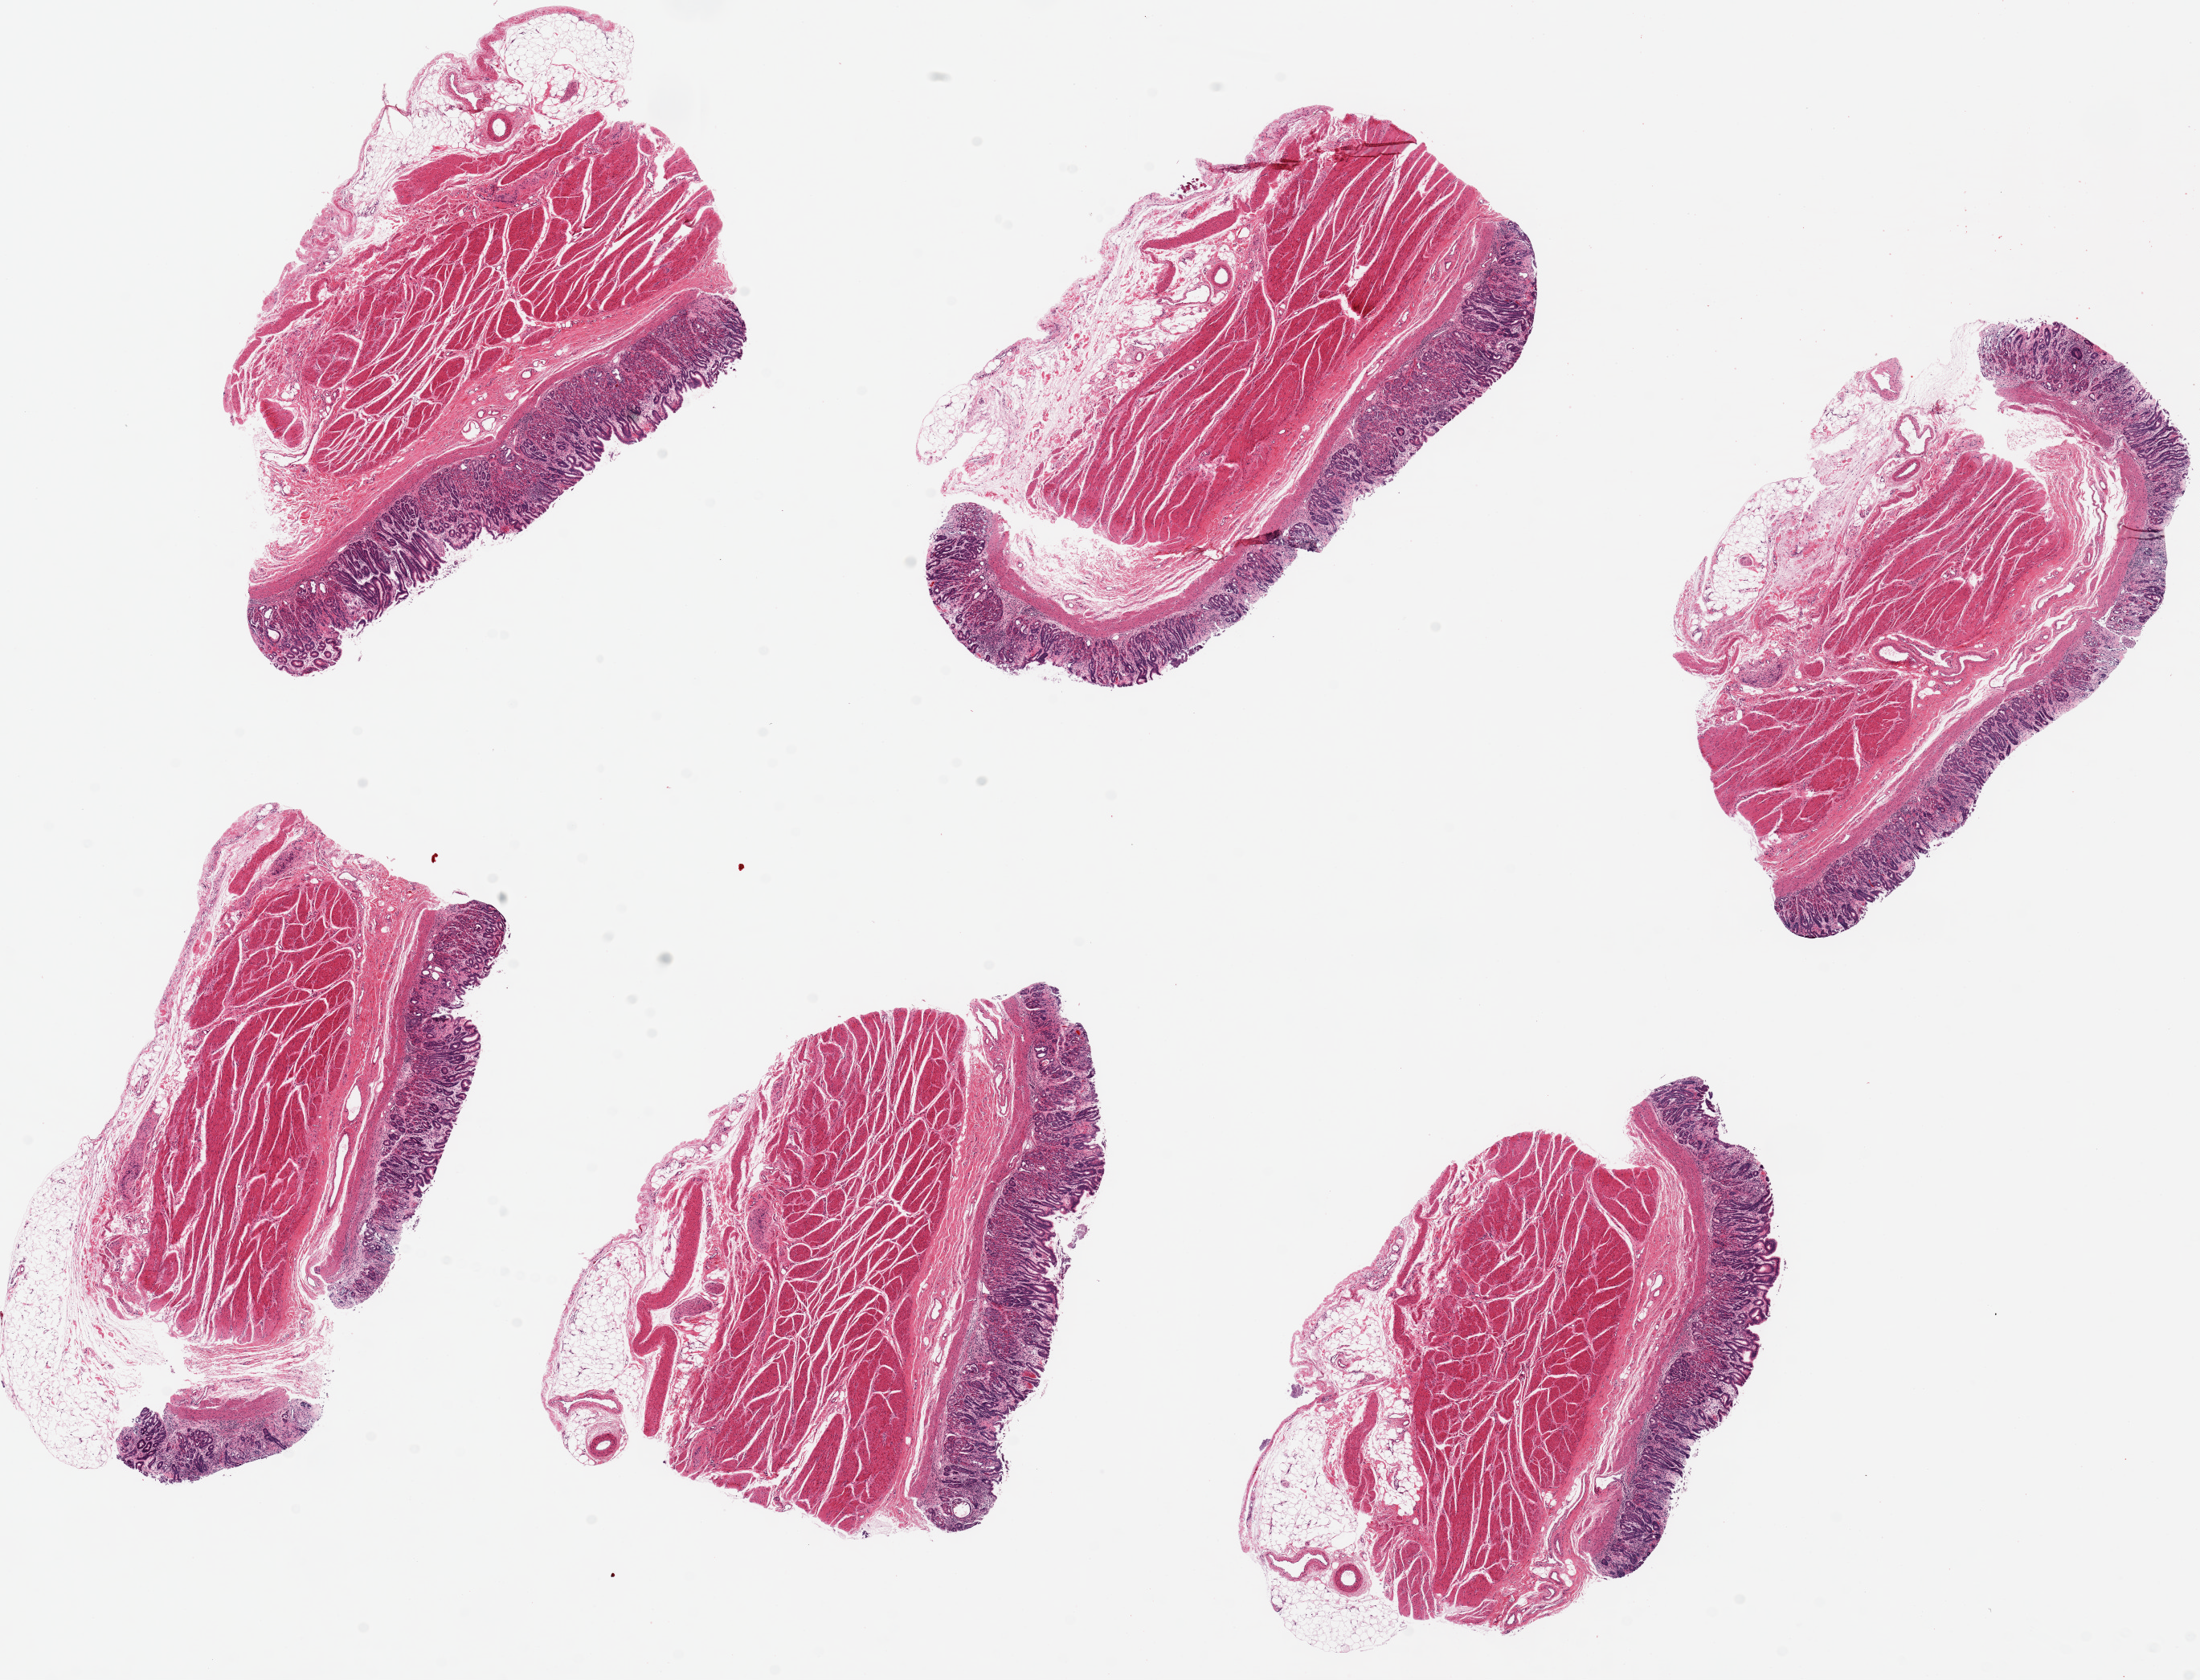
Digitized hematoxylin and eosin (H&E)-stained section — shown as a low-resolution overview of the whole scanned area (about 21.7 x 16.5 mm, from a 20x scan). PAXgene-fixed paraffin-embedded (PFPE) section. Section of stomach (target tissue). Donor tissue sample. Male donor.
Pathologist's review note for this sample: 6 pieces, up to 7x6mm; fundic mucosa, chronic gastritis with atrophy, no intestinal metaplasia.